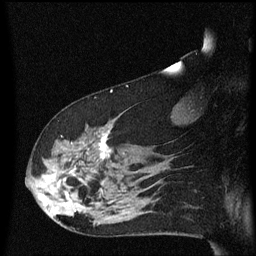
Breast MRI (dynamic contrast-enhanced), one sagittal slice; position 40 of 60 along the scan axis; dynamic contrast-enhanced series, image 2 of 3 at this slice position (ordered by acquisition); 1.5 T; TE 4.2 ms, TR 8.4 ms; 2 mm slice thickness; 256 × 256 image matrix, field of view 200 × 200 mm. Patient: female, 48 years.
Annotated regions visible in this slice (semi-automatically segmented with operator editing):
- analysis volume of interest (the breast-tissue region the enhancement analysis was run in; not a lesion): bounding box [x1, y1, x2, y2] px = [31, 118, 134, 225]
- tumour enhancement mask (voxels above the 70 % enhancement threshold inside the analysis volume of interest): [40, 130, 110, 203]